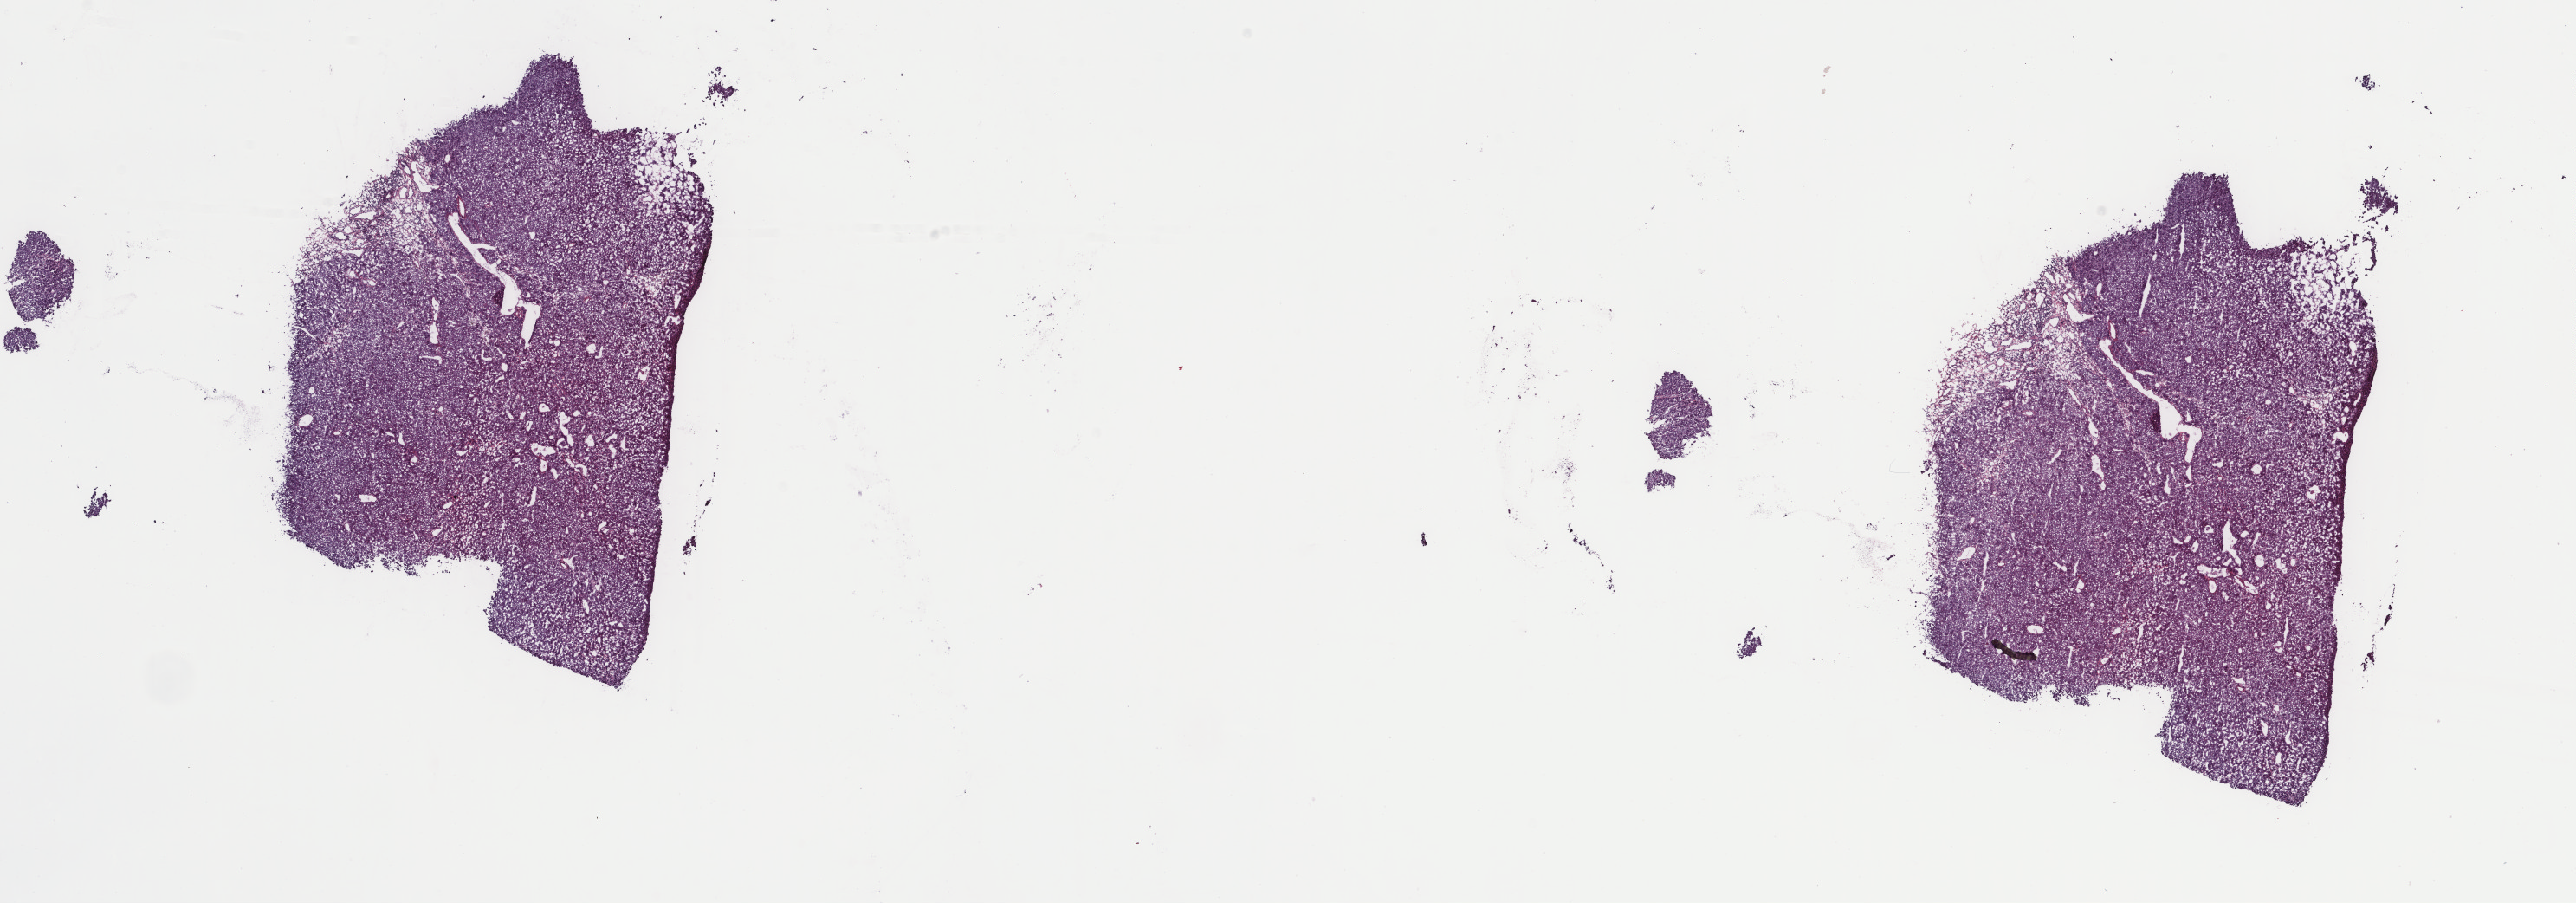
H&E-stained whole-slide image, low-resolution overview of the scanned area, about 23.6 x 8.3 mm (acquisition: 40x scan). Frozen section from the top of the tissue portion. Sample: primary tumour, liver. Patient: male, age at initial diagnosis 46 years.
Diagnosis: Hepatocellular carcinoma, NOS.